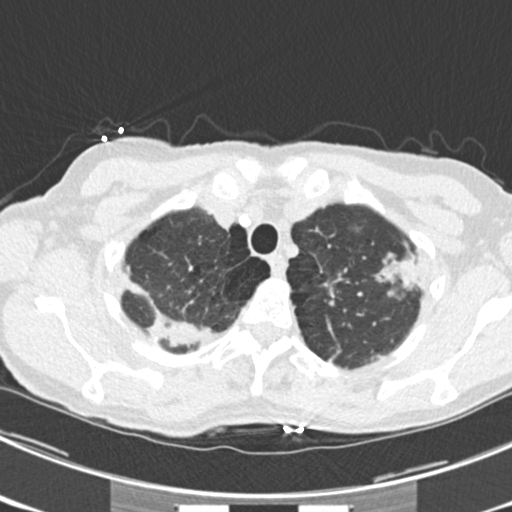
Low-dose screening chest CT, one axial slice. Reconstruction kernel B30f. 120 kVp. Lung window (W 1500 / L -600 HU). 2 mm slice thickness. 512 × 512 image matrix.
Structures marked on this image (expert manual segmentation):
- lesion 1 (tumor, upper lobe of left lung): bounding box (x1, y1, x2, y2) in pixels: (381, 257, 415, 287)
- lesion 4 (tumor, upper lobe of right lung): (151, 316, 204, 345)